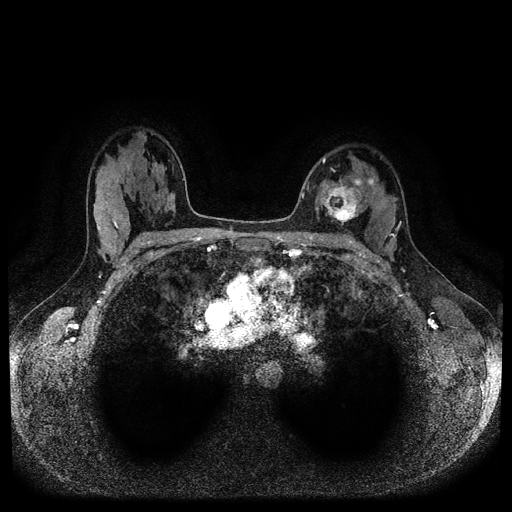
Breast MRI (dynamic contrast-enhanced, multi-phase), one axial slice. Slice 66 of 116 in the series (ordered by position). Dynamic contrast-enhanced series, time point 2 of 5 at this slice position (early post-contrast). 1.5 T. TE 2.6 ms, TR 5.3 ms. 2 mm slice thickness. 512 × 512 image matrix. Female patient, age 33 years.
Outlined on this slice (semi-automatically segmented with operator editing):
- breast lesion (labelled 'tumour' in the annotation; benign lesions carry a separate 'benign' label): bounding box [x1, y1, x2, y2] px = [321, 182, 361, 227]